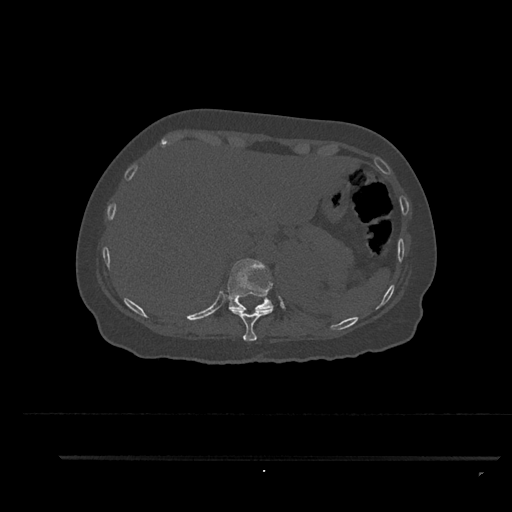
CT including the spine, one axial slice. Reconstruction kernel Br40s/3. 120 kVp. Bone window (W 1800 / L 400 HU). 512 × 512 image matrix, field of view 408 × 408 mm. Patient: female, 44 years. Case-level facts recorded for this patient, not image findings: primary cancer: renal; vertebrae with lytic lesions (as recorded): L1.
Structures marked on this image (semi-automatically segmented with operator editing):
- T10 vertebra: bounding box [x1, y1, x2, y2] px = [228, 307, 273, 341]
- T11 vertebra: [227, 258, 274, 311]